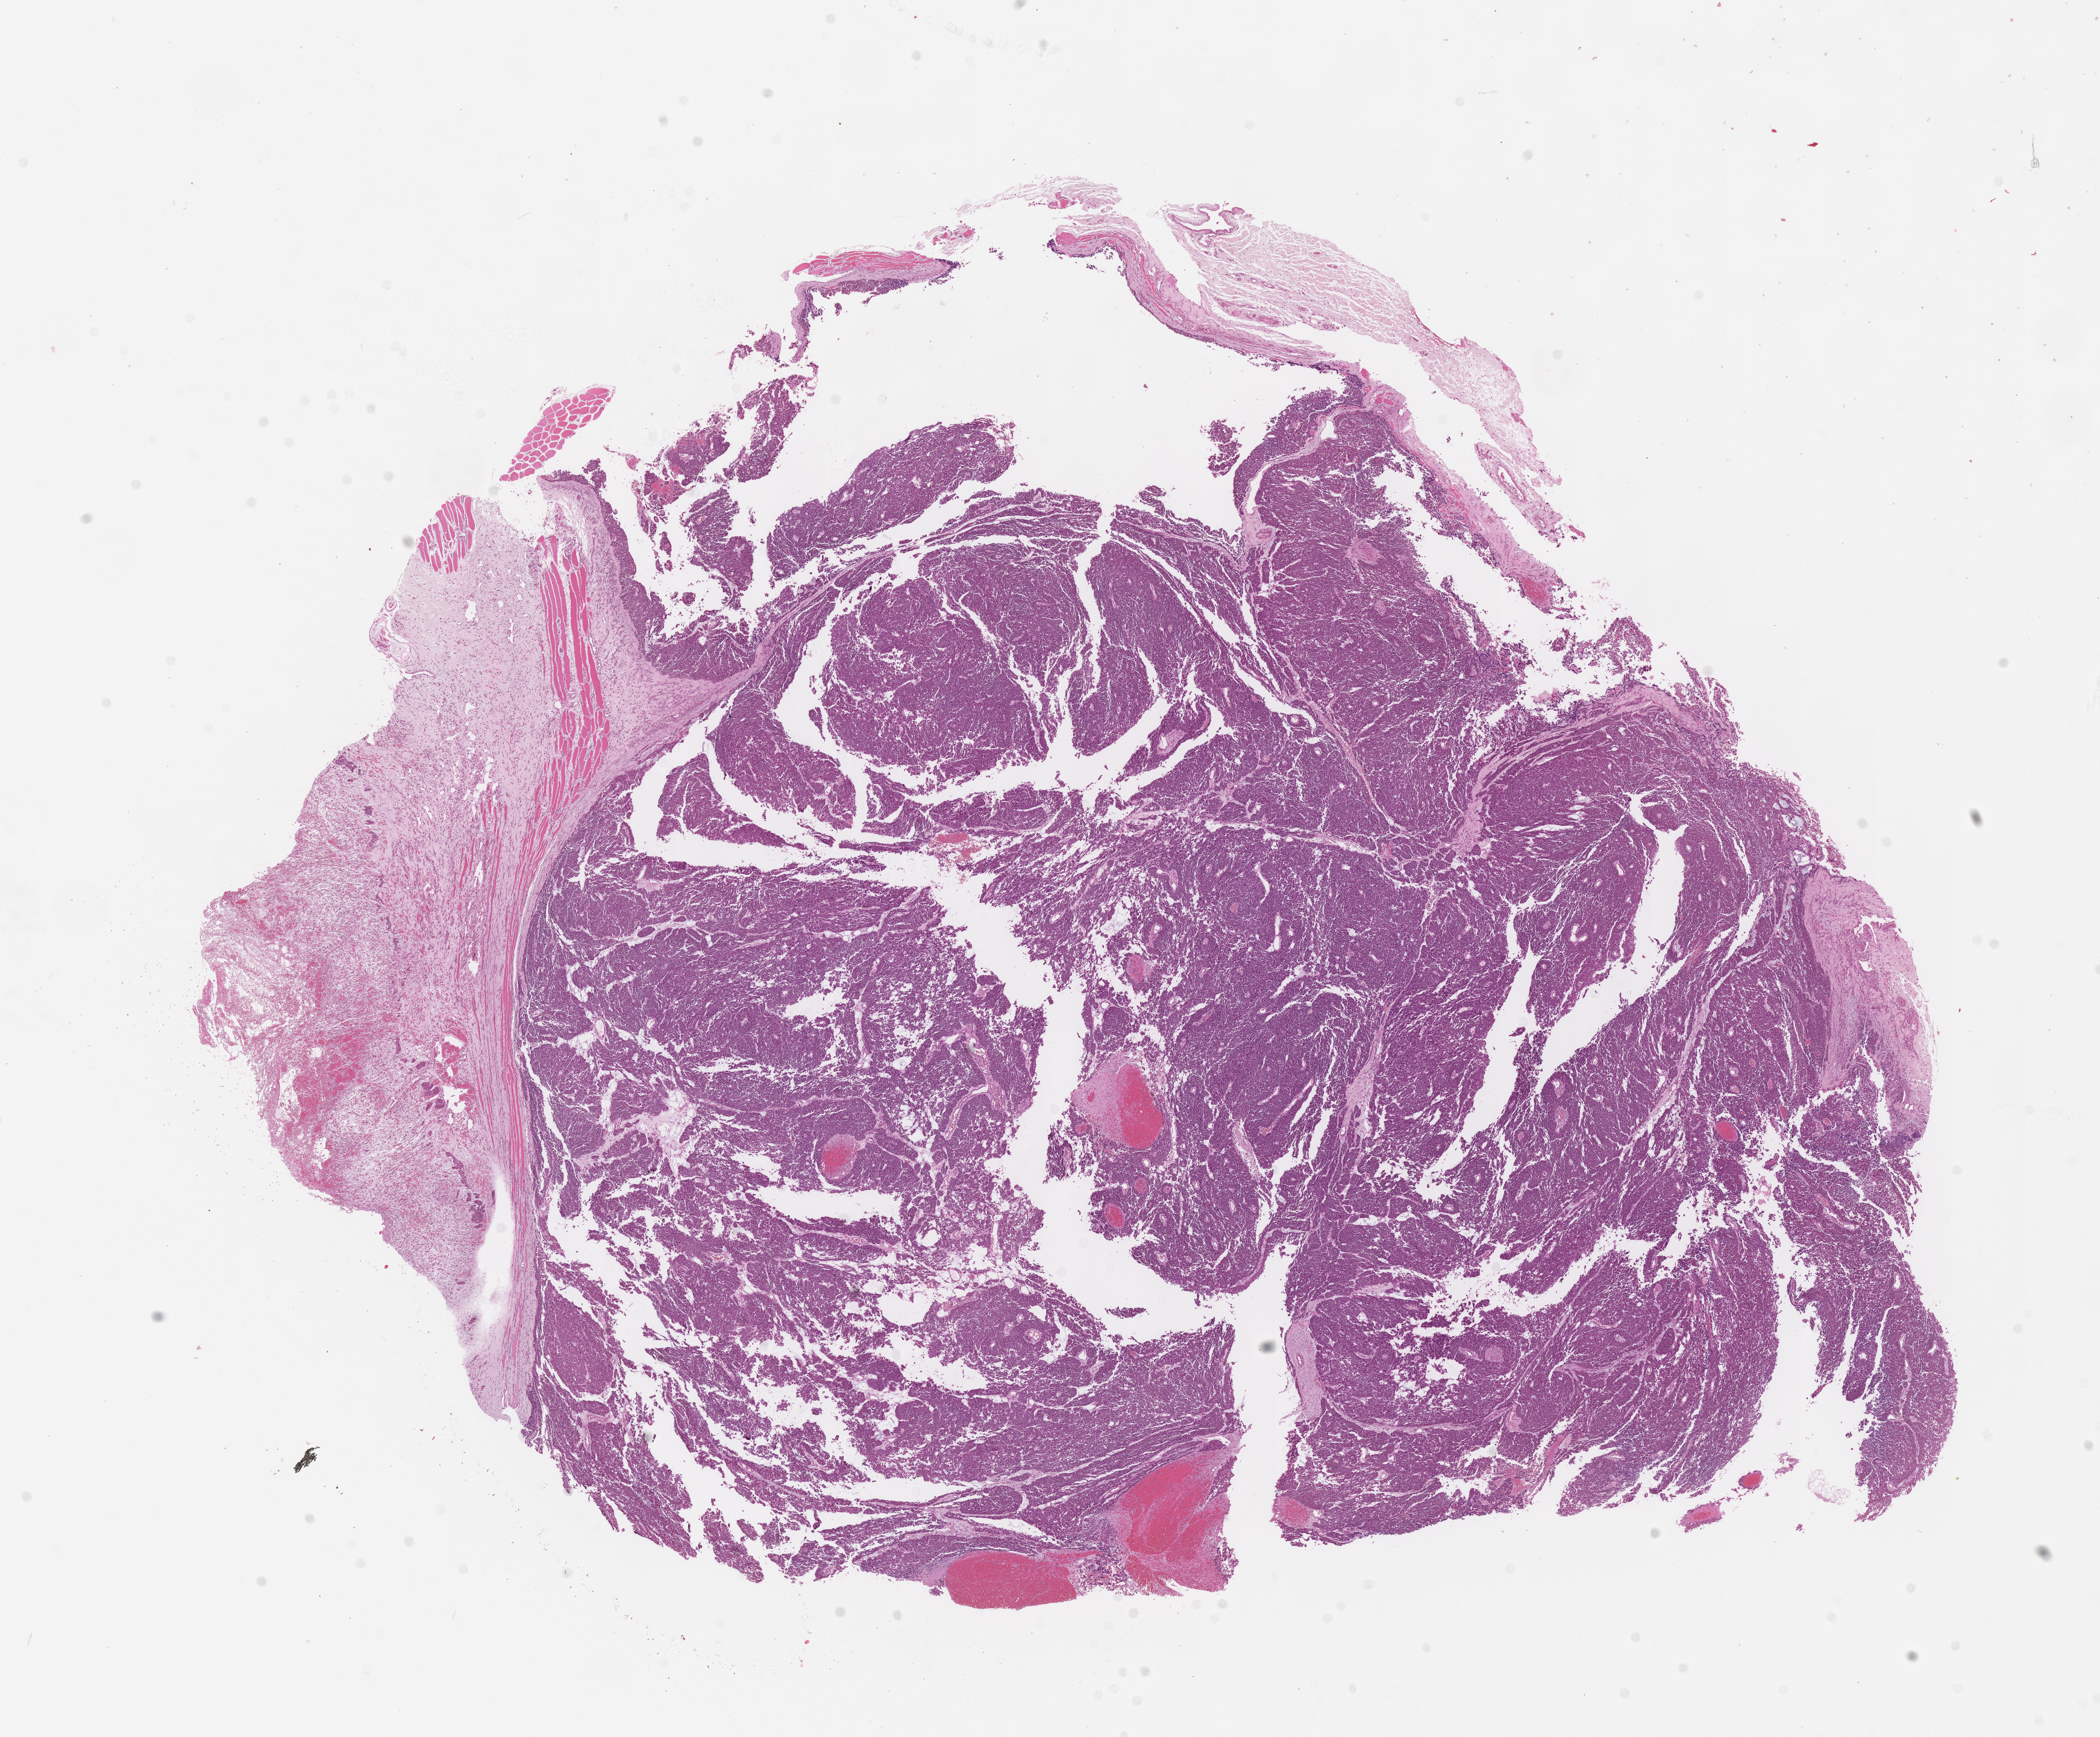
Haematoxylin and eosin whole-slide image of tumor tissue, a low-resolution overview of the entire scanned area, about 14.1 x 11.7 mm; formalin-fixed, paraffin-embedded (FFPE) tissue; sample anatomic site: soft tissue, abdomen. Patient: female, age 18.0 years at diagnosis.
Primary site (case record): abdominal wall. Diagnosis: rhabdomyosarcoma; histological classification: mixed alveolar and embryonal rhabdomyosarcoma. Metastatic status at presentation (as recorded): non-metastatic (unconfirmed). Stage (as recorded): 2.